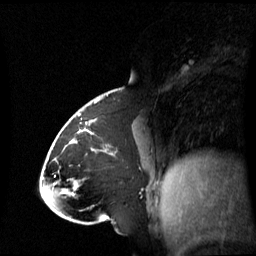
Breast MRI (dynamic contrast-enhanced), one sagittal slice. Dynamic contrast-enhanced series, image 2 of 3 at this slice position (ordered by acquisition). 1.5 T. TE 4.2 ms, TR 8.4 ms. 256 × 256 image matrix, field of view 270 × 270 mm. Female patient, age 43 years. From the clinical record (not read from this slice): setting: breast cancer imaged before/during neoadjuvant chemotherapy; receptor status: triple-negative.
Structures marked on this image (semi-automatically segmented with operator editing):
- analysis volume of interest (the breast-tissue region the enhancement analysis was run in; not a lesion): box from (x=65, y=118) to (x=143, y=198) px
- tumour enhancement mask (voxels above the 70 % enhancement threshold inside the analysis volume of interest): (x=76, y=120)–(x=96, y=143)